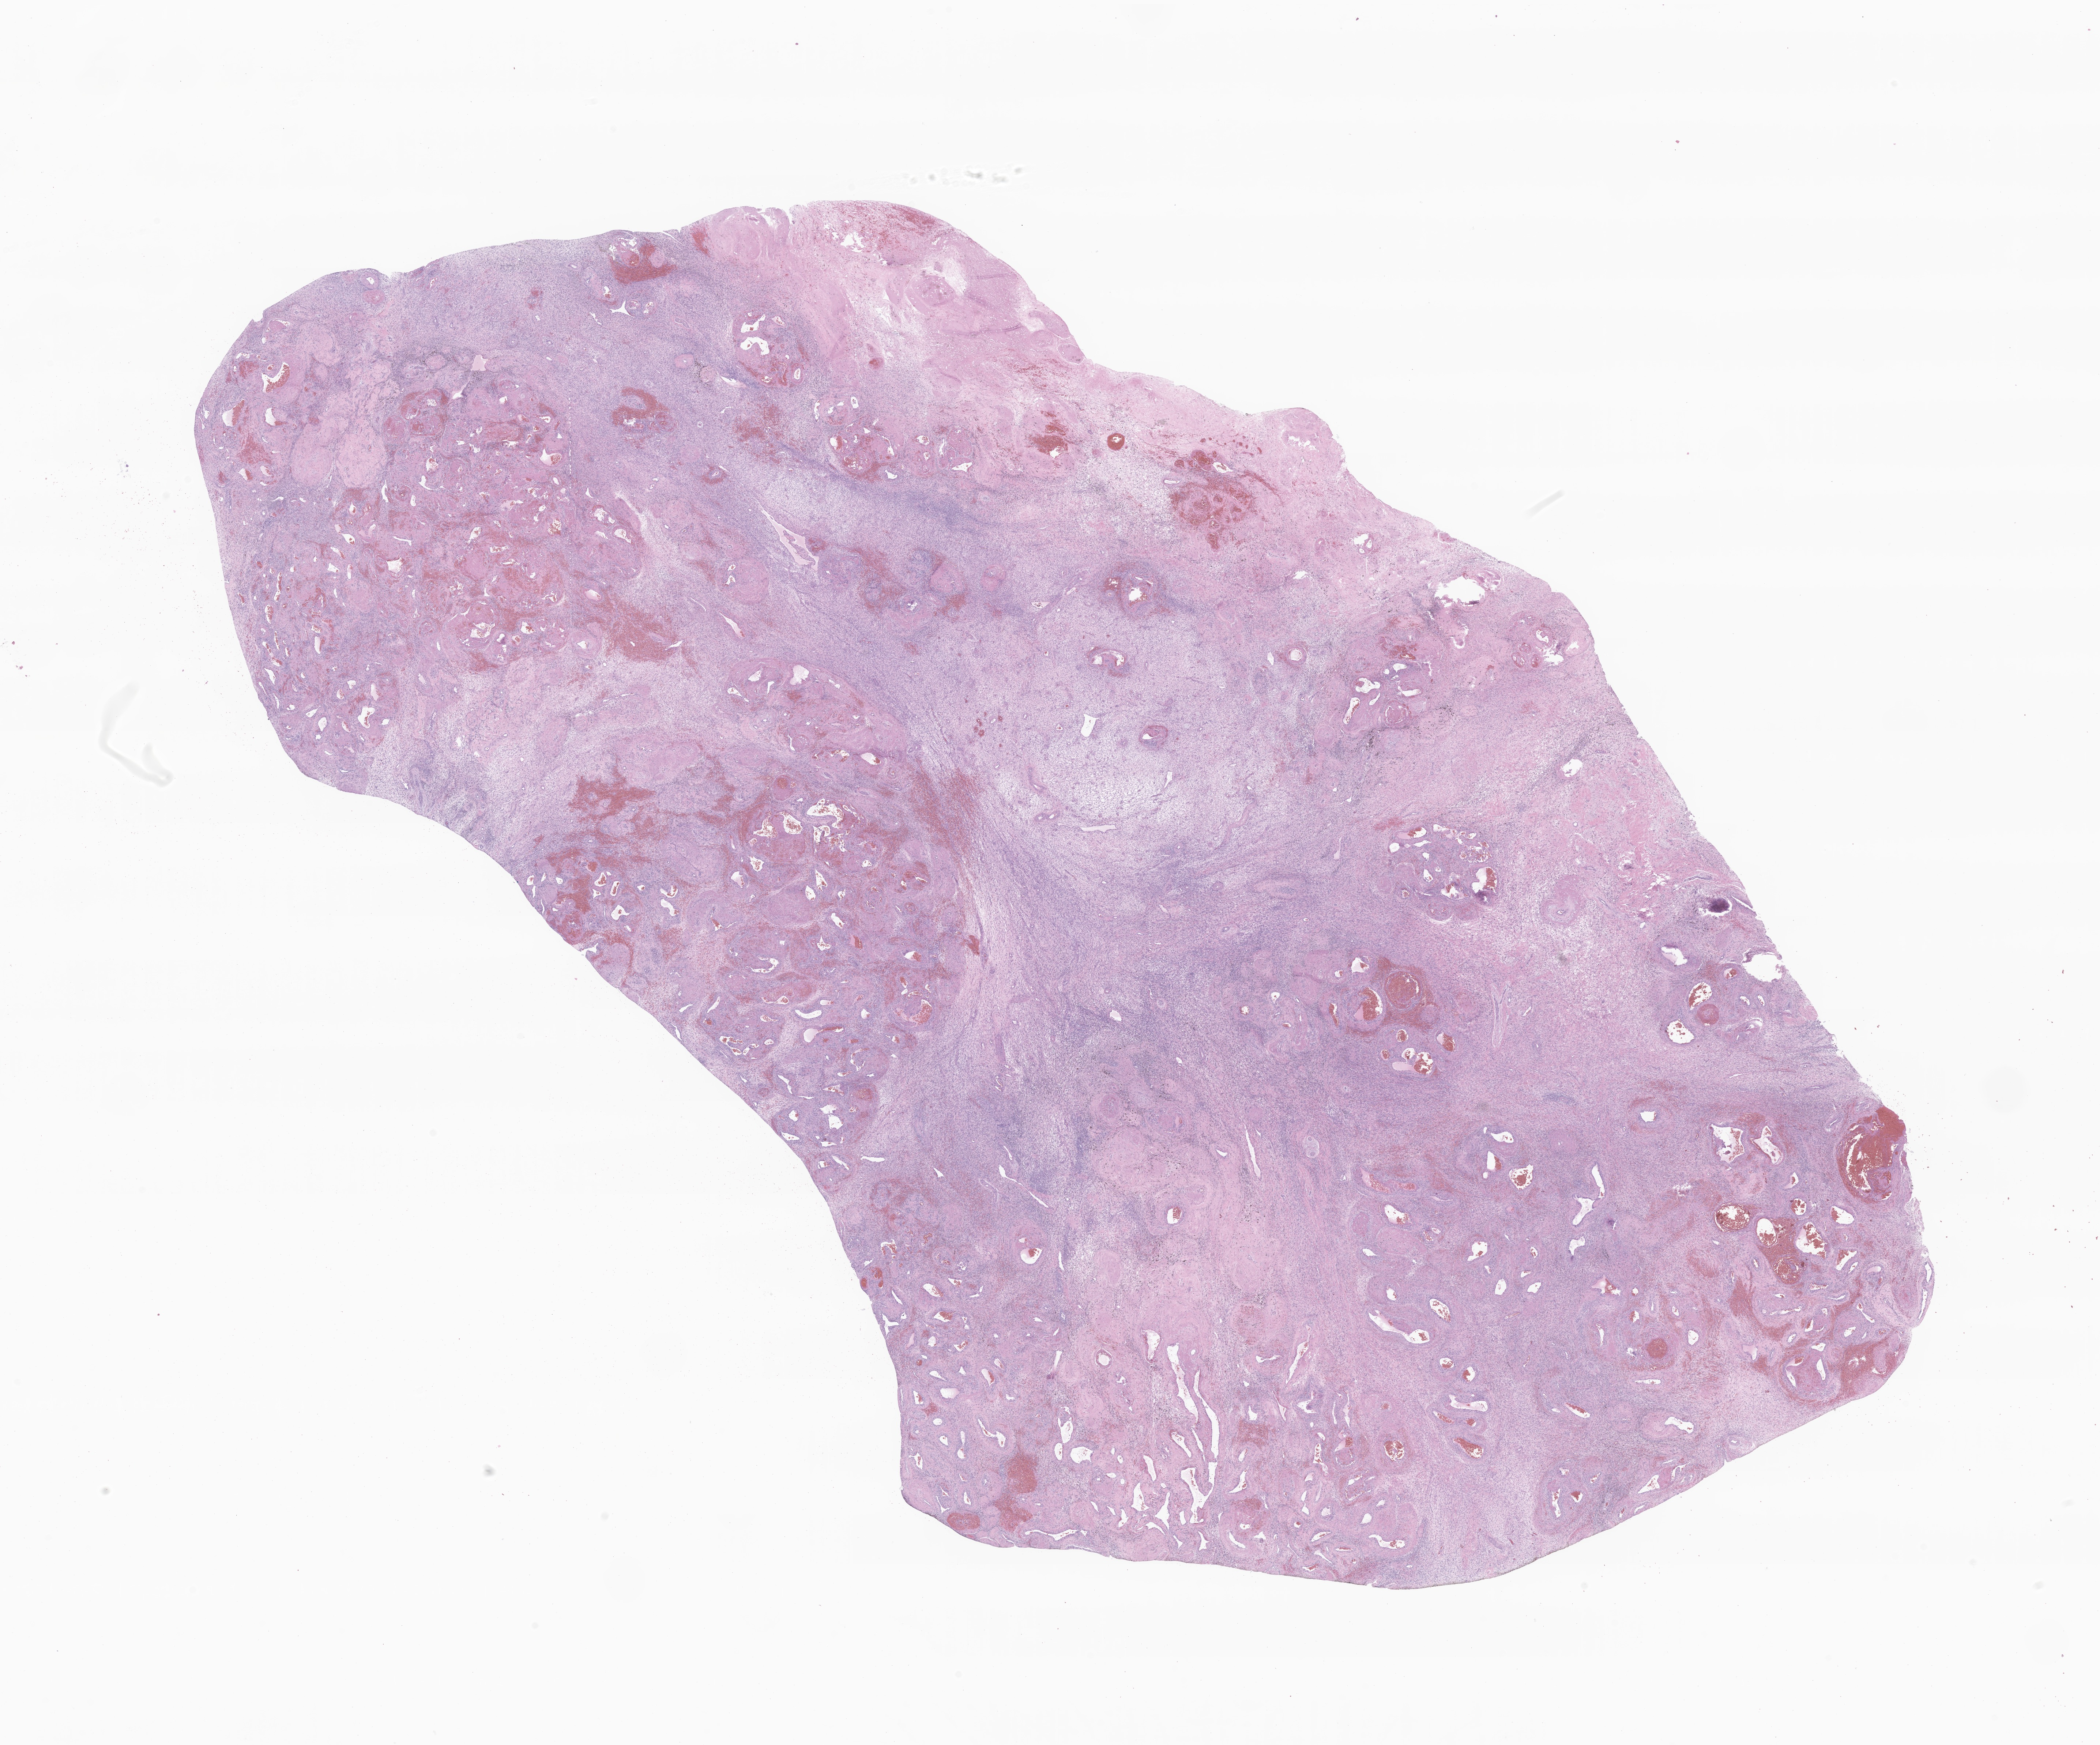
Whole-slide image, haematoxylin and eosin stain of tumor tissue from the soft tissue of lower extremity, whole scanned area (about 24.2 x 20.1 mm) shown as a low-resolution overview. Formalin-fixed paraffin-embedded section. Female patient, age 217 months (18 years 1 month).
Diagnosis: Synovial sarcoma, spindle cell.